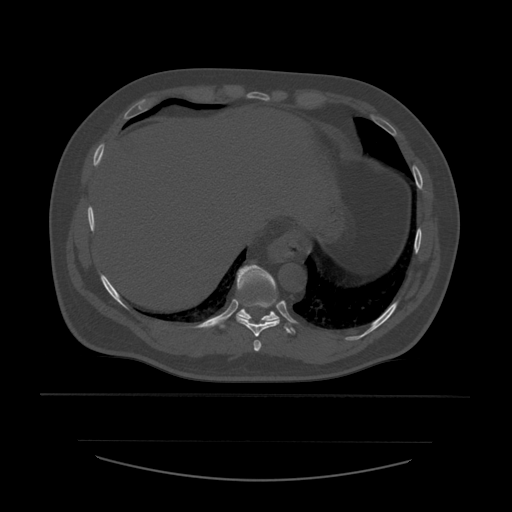
CT including the spine, one axial slice. Reconstruction kernel STANDARD. Bone window (W 1800 / L 400 HU). 512 × 512 image matrix, field of view 441 × 441 mm. Patient age 44 years. Case-level facts recorded for this patient, not image findings: primary cancer: soft tissue sarcoma.
Structures marked on this image (semi-automatic segmentation, software-assisted and operator-edited):
- T10 vertebra: bounding box <223,265,293,334> (left, top, right, bottom; pixels)
- T8 vertebra: <254,340,262,353>
- T9 vertebra: <236,265,280,337>